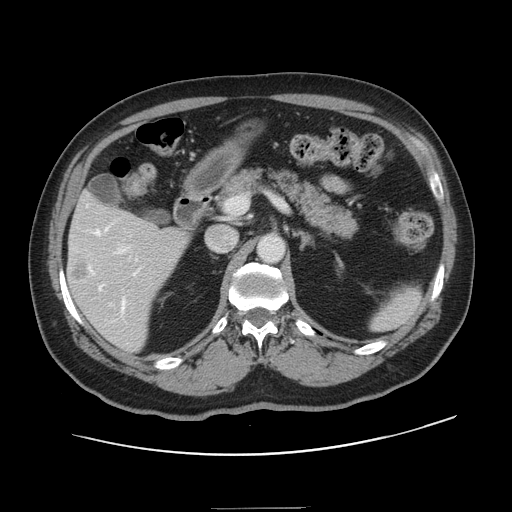
Contrast-enhanced abdominal CT, one axial slice. Position 77 of 143 along the scan axis. 120 kVp. Intravenous contrast given. Soft-tissue window (W 400 / L 40 HU). 2.5 mm slice thickness. 512 × 512 image matrix, field of view 402 × 402 mm. Male patient, age 62 years. Case-level facts recorded for this patient, not image findings: diagnosis: colorectal cancer liver metastases, imaged before liver resection; multiple liver metastases: yes; largest metastasis: 2.7 cm; disease in both lobes: no.
Annotated regions visible in this slice (manually delineated by an expert):
- hepatic veins: box from (x=87, y=205) to (x=139, y=312) px
- liver: (x=68, y=196)–(x=186, y=351)
- planned liver remnant (the part of the liver to remain after resection): (x=73, y=196)–(x=136, y=228)
- portal vein (with intrahepatic branches): (x=110, y=246)–(x=128, y=322)
- liver metastasis: (x=74, y=263)–(x=89, y=281)